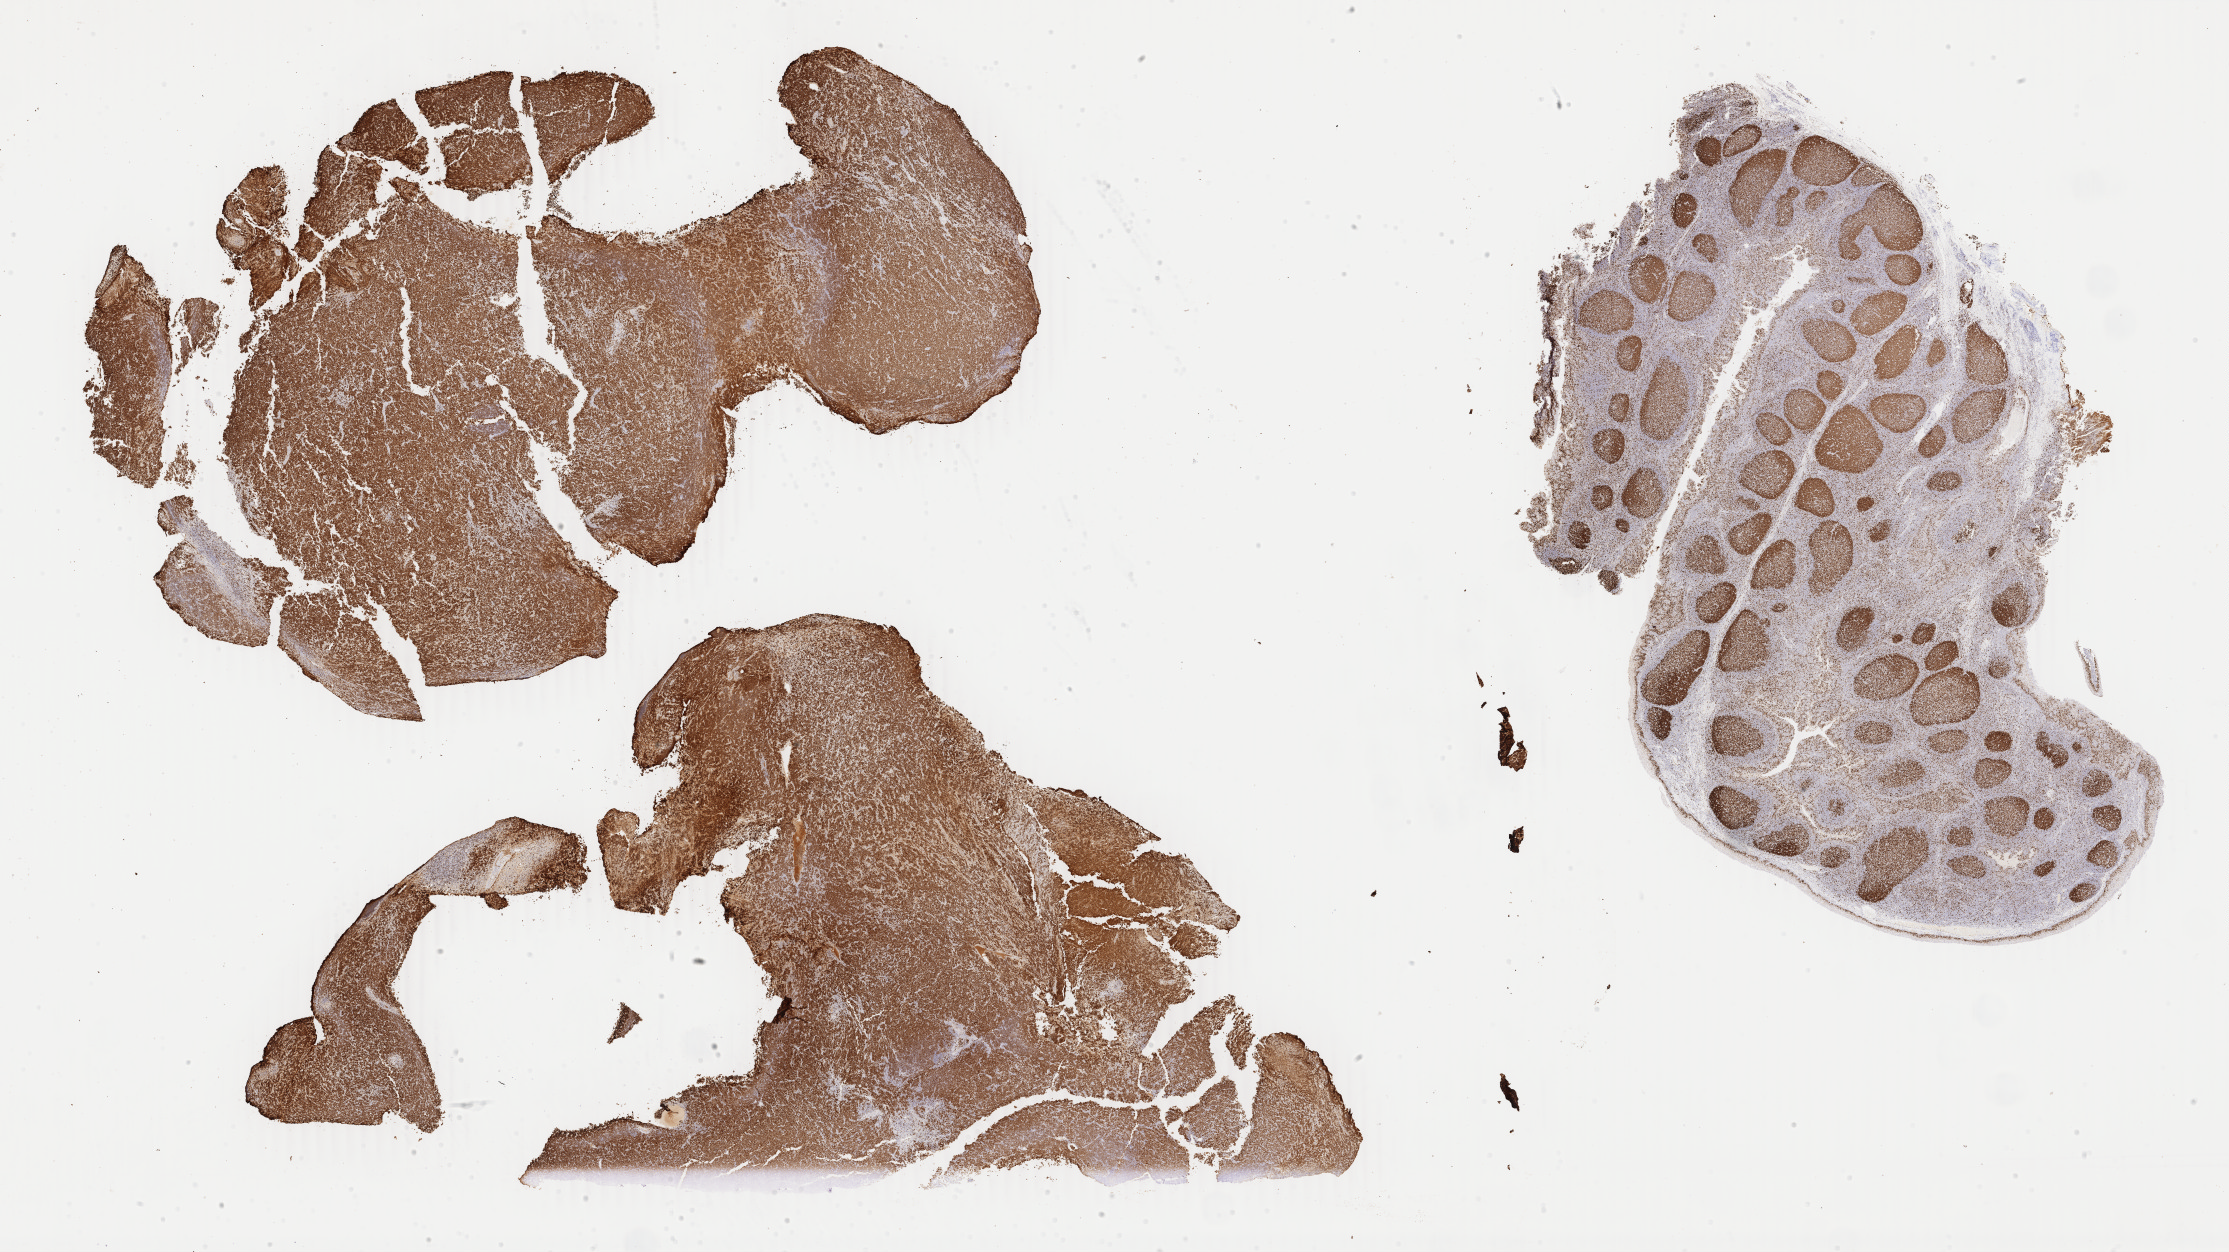
Whole-slide image, immunohistochemical stain for Ki-67, low-resolution overview of the scanned area, about 35.5 x 19.9 mm; specimen: tumor tissue; anatomic site: liver. Patient: male, aged 45.
Diagnosis: Diffuse large B-cell lymphoma, NOS.